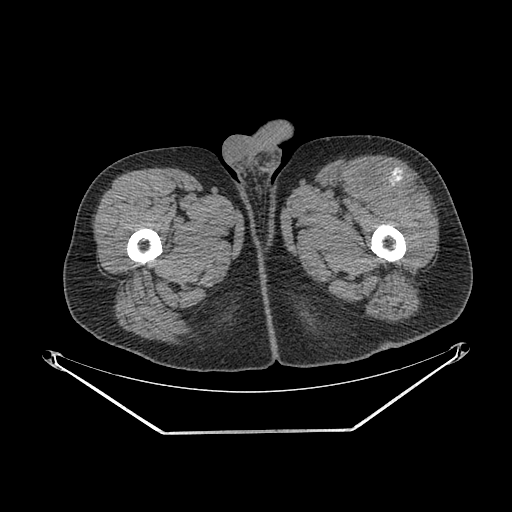
CT of an extremity soft-tissue mass (from a PET/CT study), one axial slice; 140 kVp; soft-tissue window (W 400 / L 40 HU); 512 × 512 image matrix, field of view 500 × 500 mm. Male patient. From the clinical record (not read from this slice): histological type: extraskeletal osteosarcoma; grade: high; site of the primary tumour: thigh.
Structures marked on this image (expert contour drawn on MRI and transferred to this co-registered scan by the dataset authors):
- gross tumour volume (mass): box from (x=368, y=169) to (x=419, y=195) px